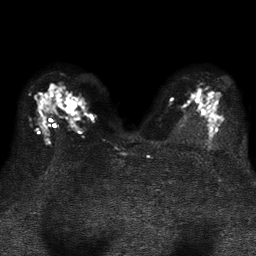
Breast MRI, one axial slice. Slice 23 of 37 in the series (ordered by position). Diffusion-weighted series; image 2 of 4 stored at this slice position (different b-values; order by instance number). 1.5 T. 256 × 256 image matrix, field of view 320 × 320 mm. Female patient.
Outlined on this slice (manually delineated by an expert):
- tumour on diffusion-weighted imaging: bounding box [x1, y1, x2, y2] px = [65, 98, 75, 111]